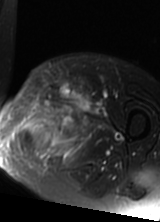
MRI of an extremity soft-tissue mass, one axial slice. Slice 44 of 69 in the series (ordered by position). T2-weighted fat-saturated. MR volume resampled by the dataset authors to the PET/CT grid (not the native acquisition matrix). 160 × 222 image matrix, field of view 156 × 217 mm. Female patient. Case-level facts recorded for this patient, not image findings: histological type: pleomorphic leiomyosarcoma; grade: high; site of the primary tumour: left thigh.
Structures marked on this image (expert contour drawn on MRI and transferred to this co-registered scan by the dataset authors):
- gross tumour volume including surrounding oedema: bounding box <16,86,94,162> (left, top, right, bottom; pixels)
- gross tumour volume (mass): <43,86,83,130>